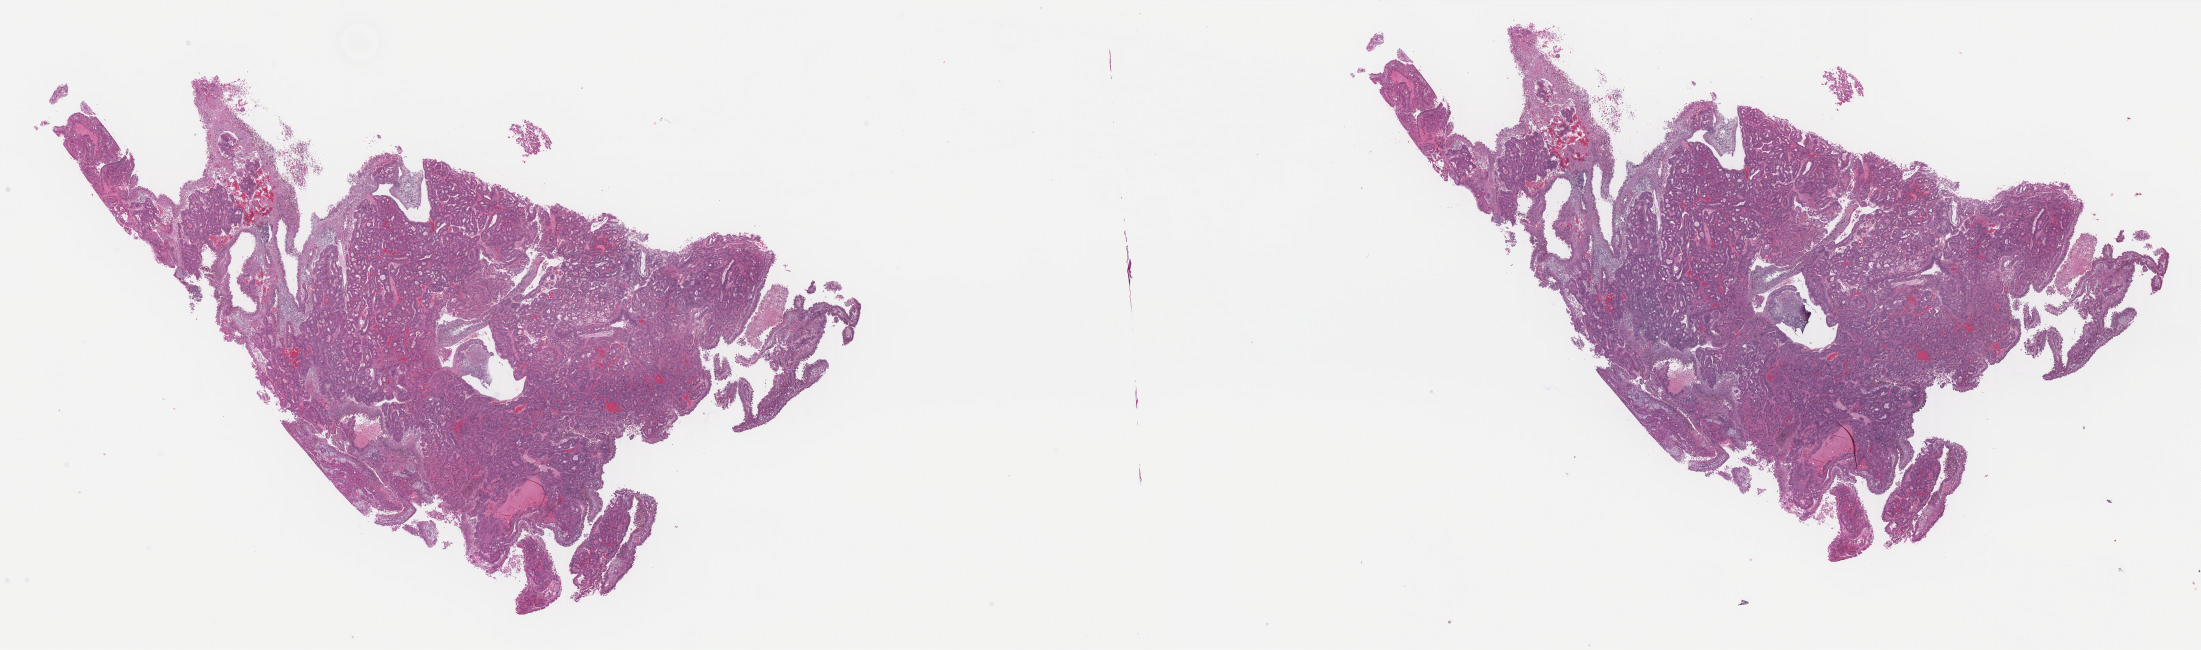
H&E whole-slide image, shown as a low-resolution overview of the whole scanned area (about 34.8 x 10.3 mm, acquisition: 40x scan); formalin-fixed paraffin-embedded (FFPE) diagnostic section; sample: primary tumour, kidney. Patient: male, age at initial diagnosis 79 years.
• AJCC pathologic stage: I (7th edition)
• diagnosis: Papillary adenocarcinoma, NOS
• laterality: left
• TNM: T1b NX MX